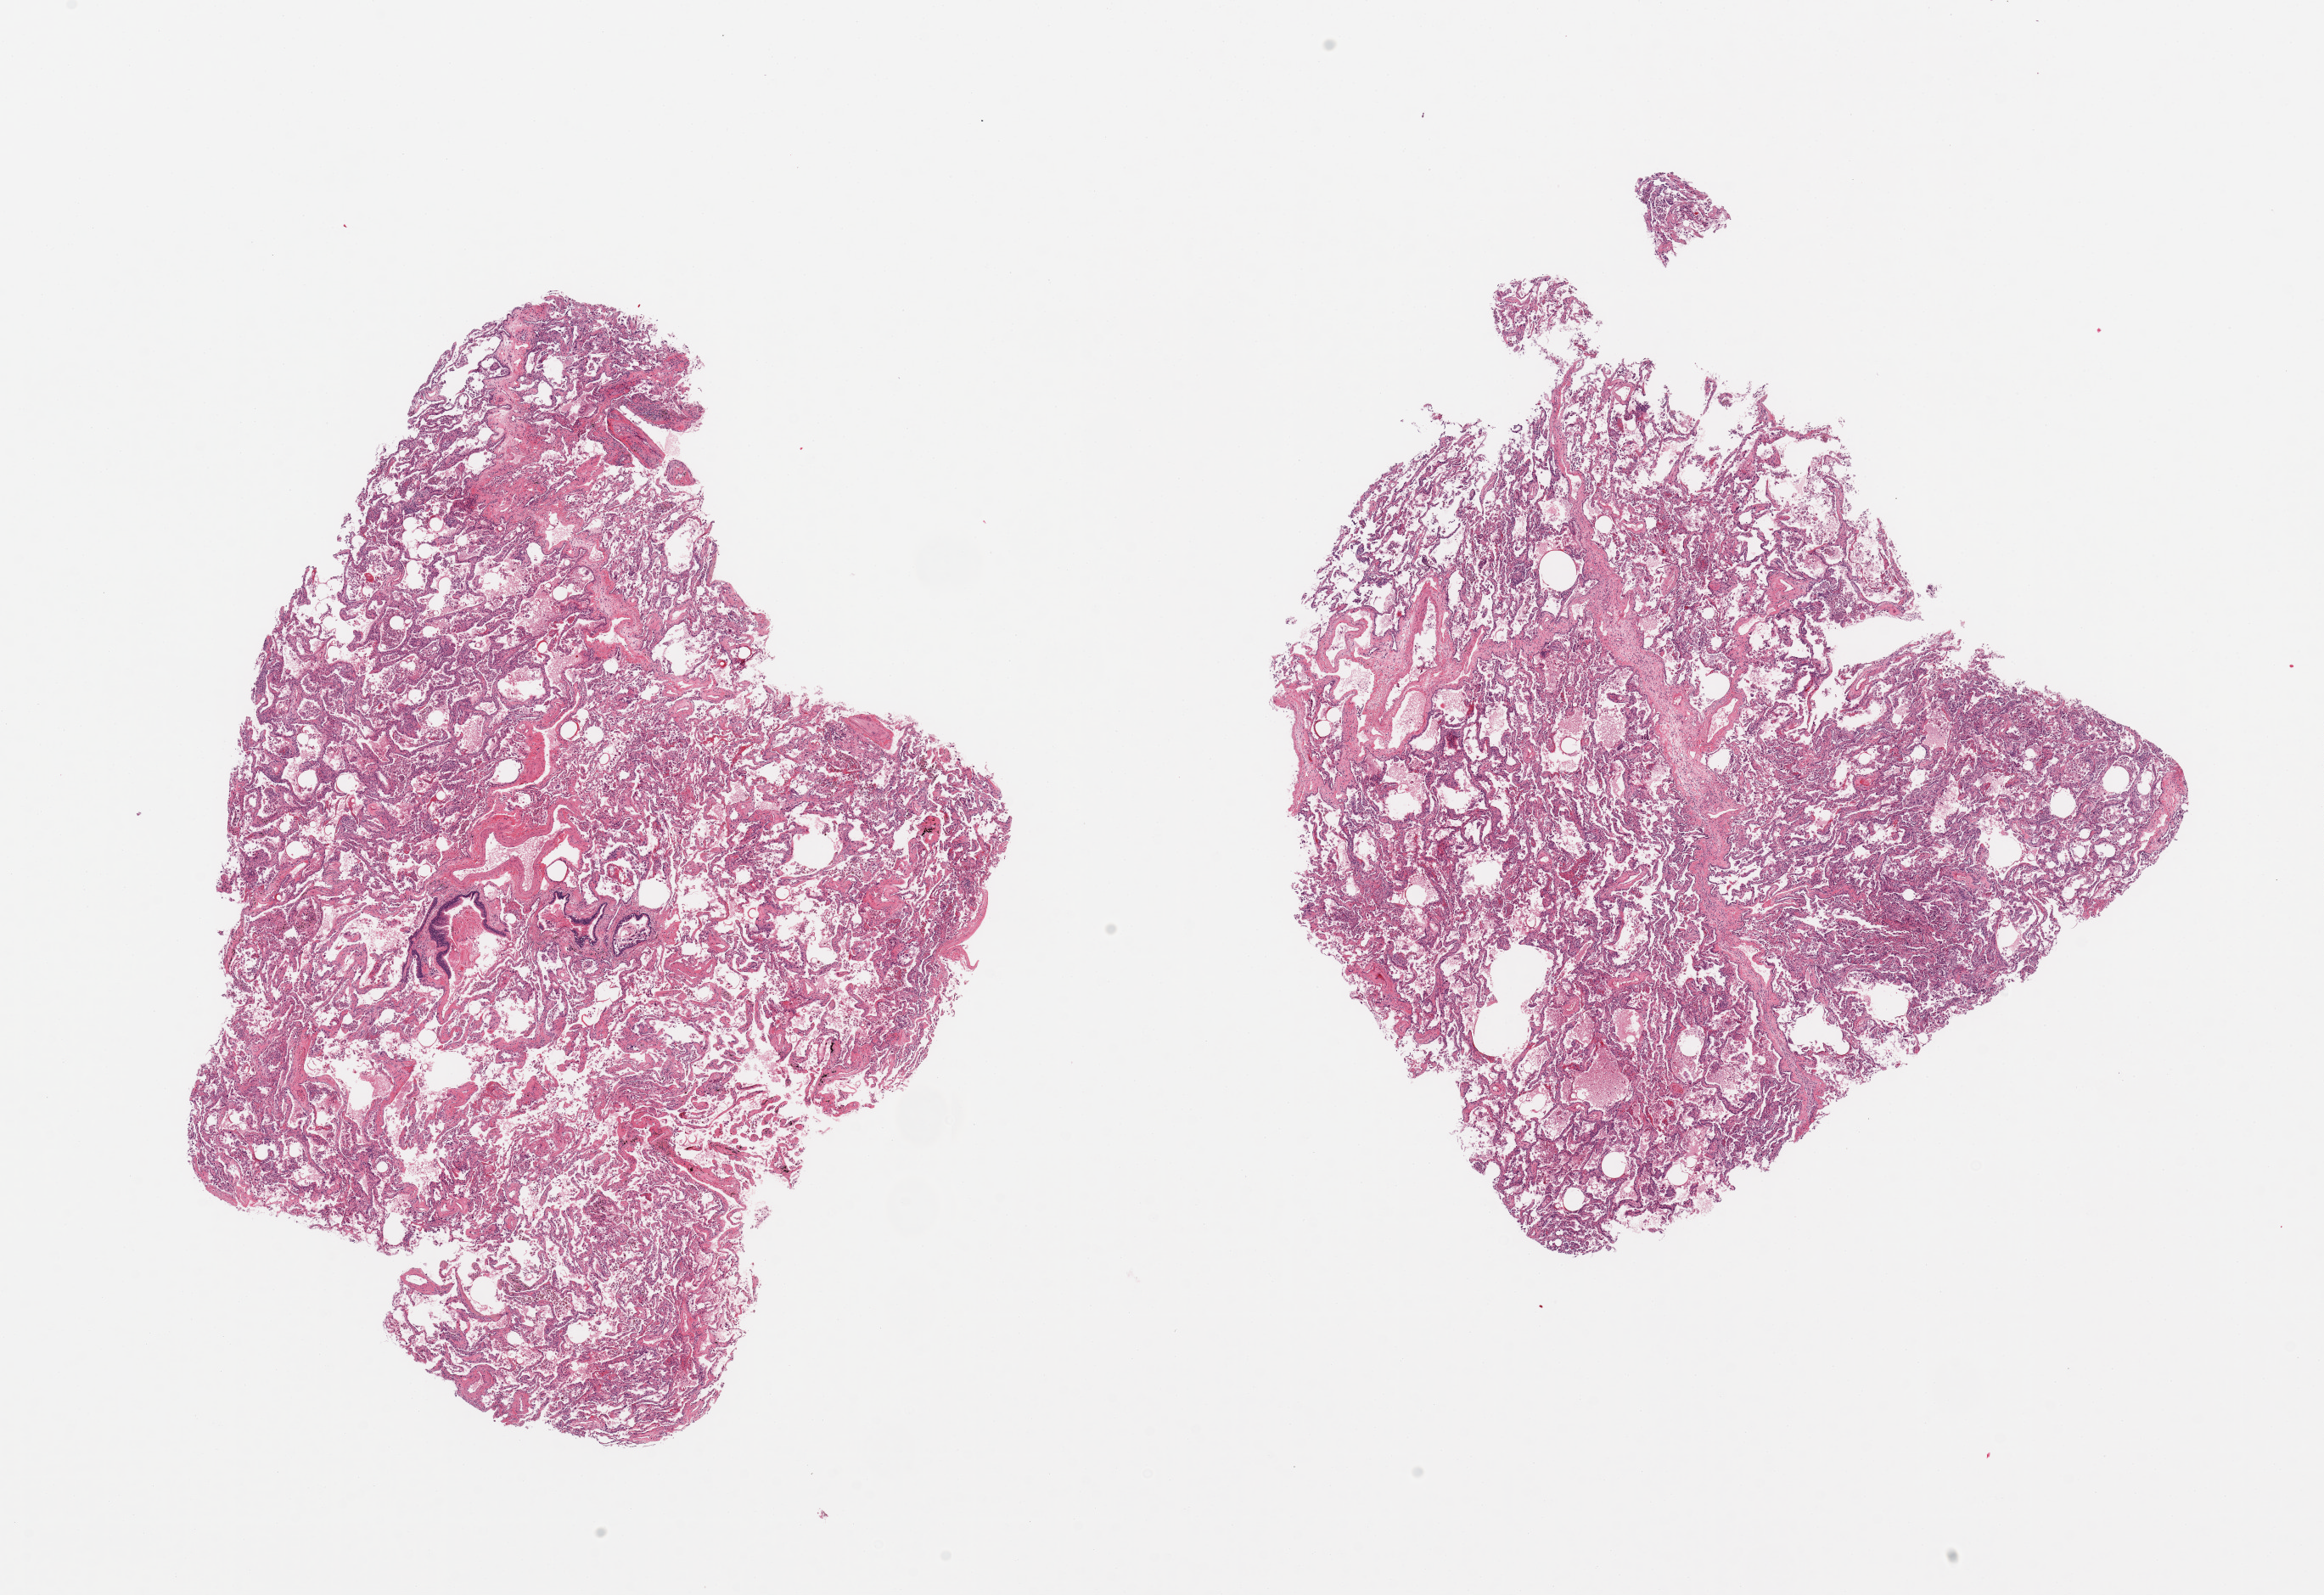
H&E whole-slide image — low-resolution overview of the scanned area, about 21.7 x 14.9 mm, PAXgene-fixed, paraffin-embedded tissue, target tissue: lung, donor tissue sample. Donor: male.
Pathologist's review note for this sample: 2 pieces; moderate diffuse fibrosis, emphysema.